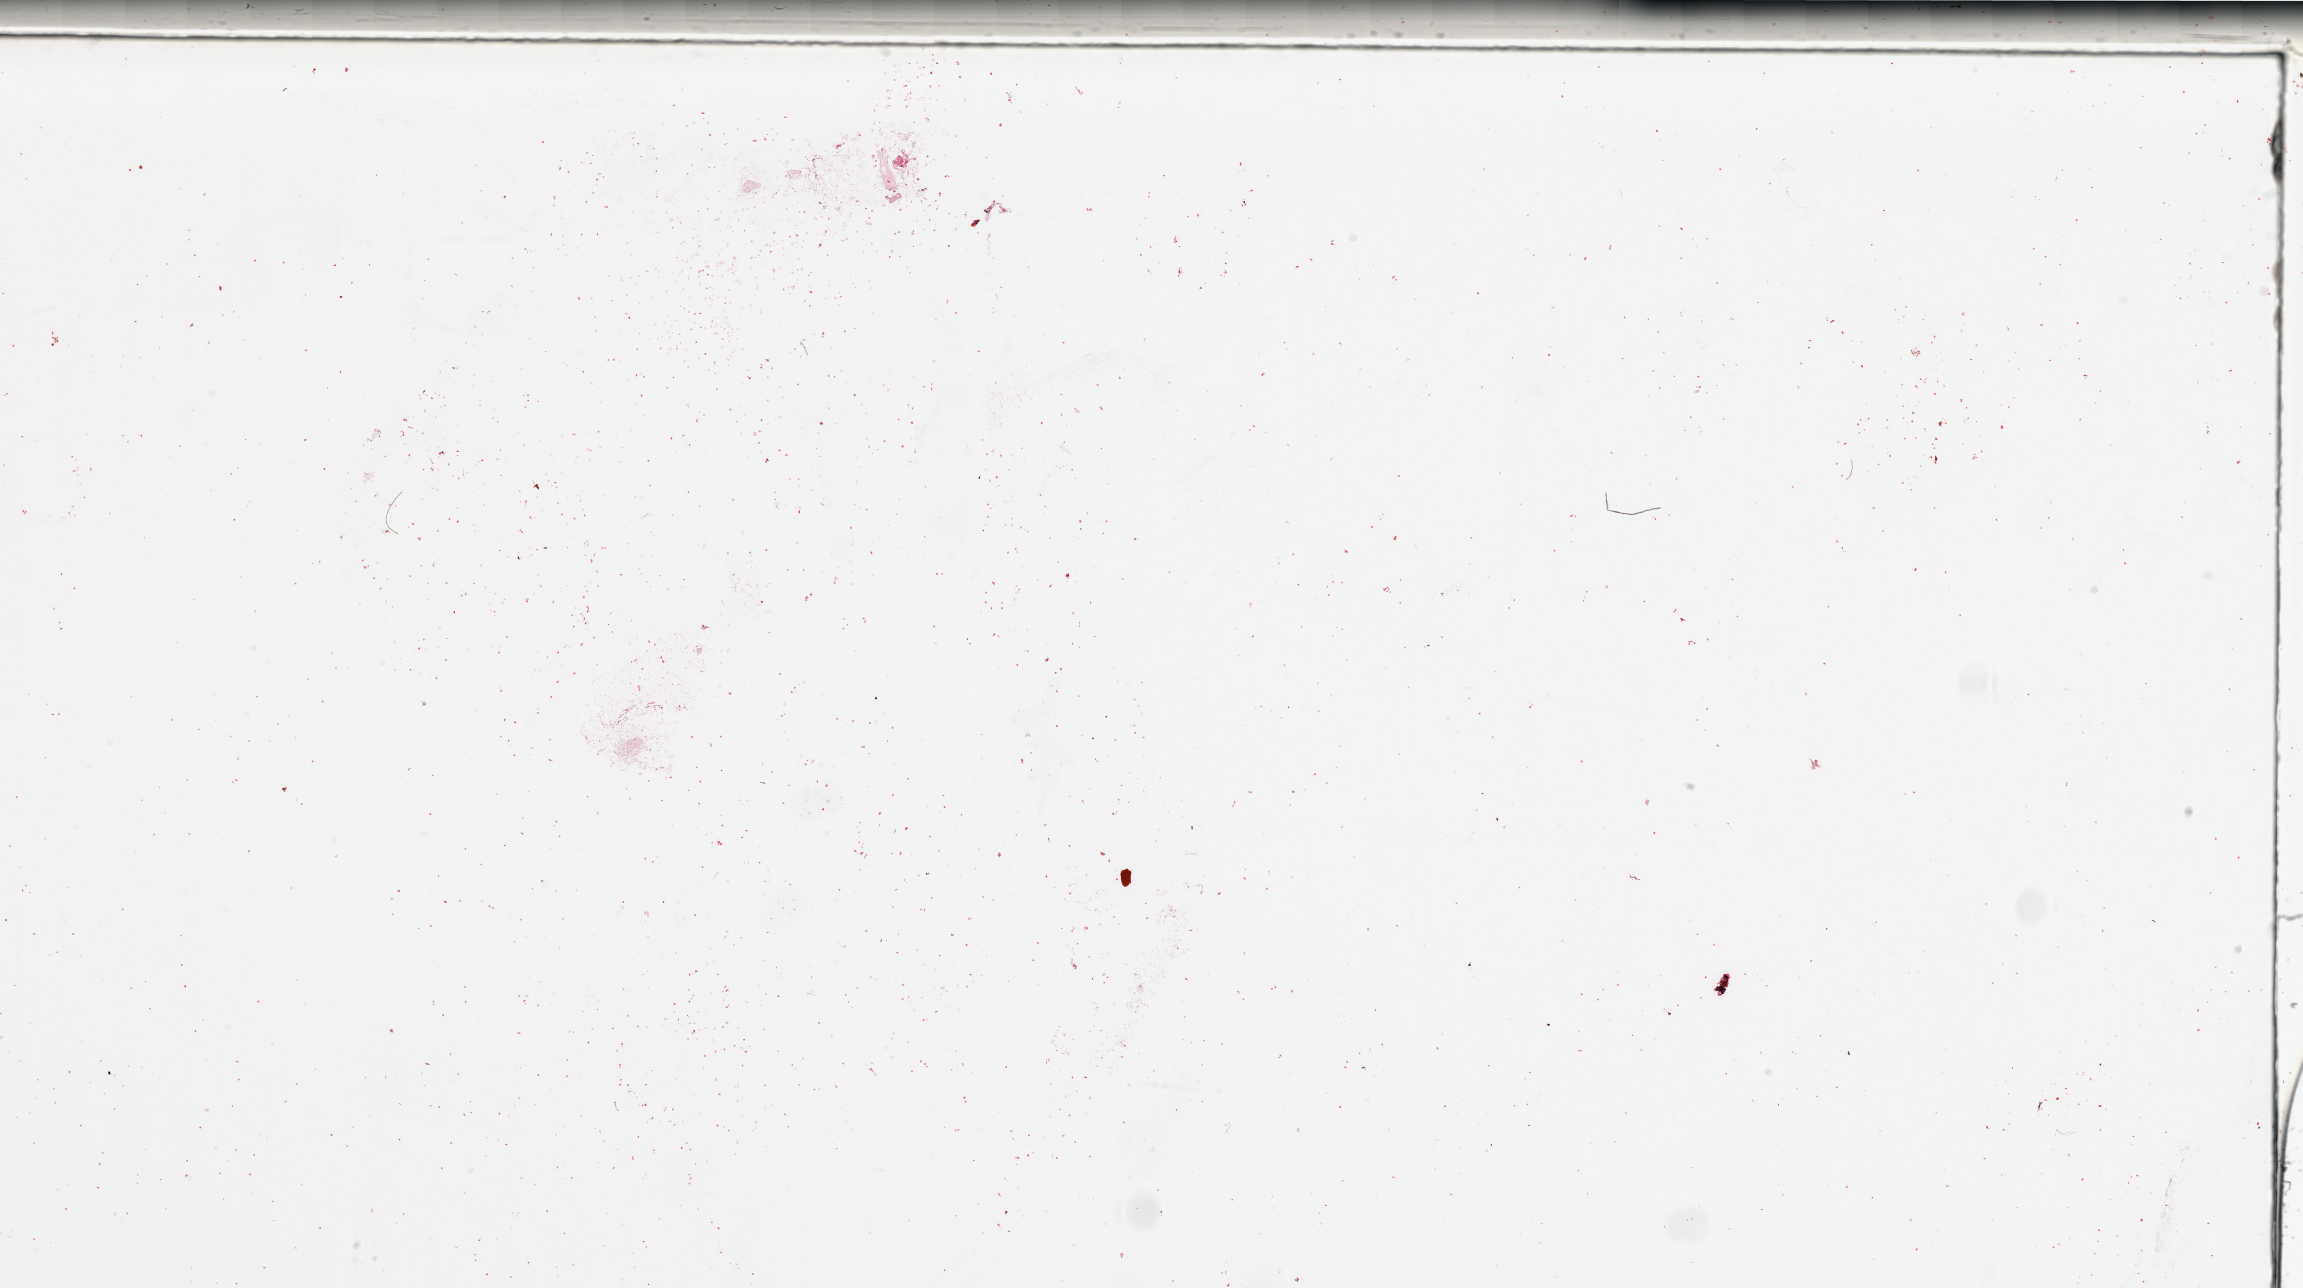
Digitized H&E-stained tissue section (whole slide), a low-resolution overview of the entire scanned area, about 36.4 x 20.4 mm (slide scanned at 20x), normal (non-tumour) tissue sample, sampled site: lymph node. Patient: male, age 76 years.
This section: normal (non-tumour) tissue from the same patient. Patient diagnosis: Malignant melanoma, NOS.